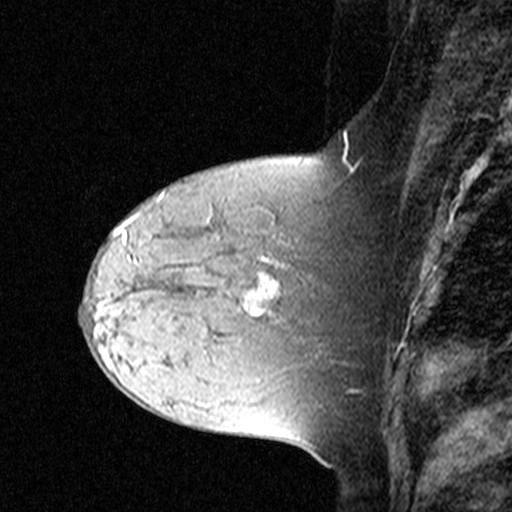
Breast MRI (dynamic contrast-enhanced), one sagittal slice; slice 15 of 44 in the series (ordered by position); dynamic contrast-enhanced study with each time point stored as its own series, time point 2 of 3 at this slice position (early post-contrast, ordered by acquisition time); 1.5 T; TE 4.5 ms, TR 11 ms; 3 mm slice thickness; 512 × 512 image matrix. Female patient, age 44 years. From the clinical record (not read from this slice): setting: breast cancer imaged before/during neoadjuvant chemotherapy; receptor status: triple-negative.
Annotated regions visible in this slice (semi-automatic segmentation, software-assisted and operator-edited):
- analysis volume of interest (the breast-tissue region the enhancement analysis was run in; not a lesion): bounding box [x1, y1, x2, y2] px = [132, 212, 309, 331]
- tumour enhancement mask (voxels above the 90 % enhancement threshold inside the analysis volume of interest): [132, 219, 279, 315]